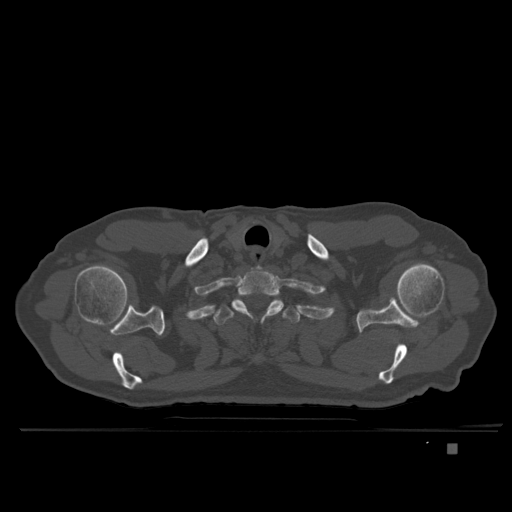
CT including the spine, one axial slice; position 320 of 435 along the scan axis; bone window (W 1800 / L 400 HU); 1.5 mm slice thickness; 512 × 512 image matrix, field of view 434 × 434 mm. Male patient, age 73 years. Case-level facts recorded for this patient, not image findings: primary cancer: skin.
Outlined on this slice (semi-automatically segmented with operator editing):
- T1 vertebra: bounding box [x1, y1, x2, y2] px = [232, 268, 284, 319]
- T2 vertebra: [214, 298, 300, 325]